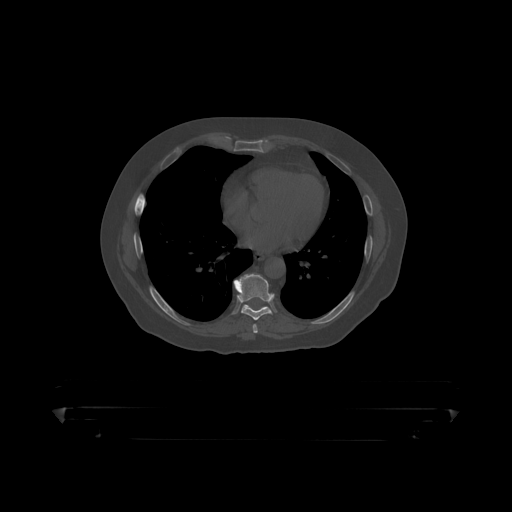
CT including the spine, one axial slice. Bone window (W 1800 / L 400 HU). 512 × 512 image matrix, field of view 650 × 650 mm. Patient: male, 60 years. Case-level facts recorded for this patient, not image findings: primary cancer: prostate.
Outlined on this slice (semi-automatic segmentation, software-assisted and operator-edited):
- T8 vertebra: bounding box [x1, y1, x2, y2] px = [234, 274, 274, 319]
- T9 vertebra: [243, 305, 251, 309]